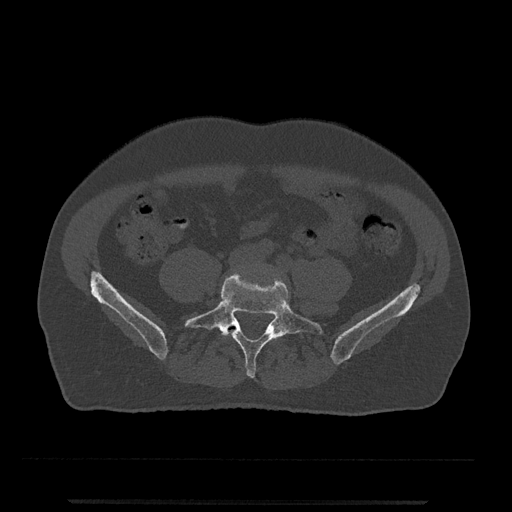
CT including the spine, one axial slice; position 81 of 797 along the scan axis; reconstruction kernel Br40s/3; 120 kVp; bone window (W 1800 / L 400 HU); 0.5 mm slice thickness; 512 × 512 image matrix, field of view 419 × 419 mm. Male patient, age 63 years. Case-level facts recorded for this patient, not image findings: primary cancer: prostate.
Outlined on this slice (semi-automatically segmented with operator editing):
- L4 vertebra: bounding box (x1, y1, x2, y2) in pixels: (227, 321, 235, 329)
- L5 vertebra: (184, 273, 323, 378)